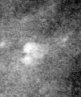
Crop from a digitized film mammogram around one marked abnormality; right breast; MLO view; BI-RADS breast density category 3 (scale 1–4).
Finding: calcifications, morphology pleomorphic, distribution clustered; BI-RADS assessment category 4; pathology (as recorded): malignant.